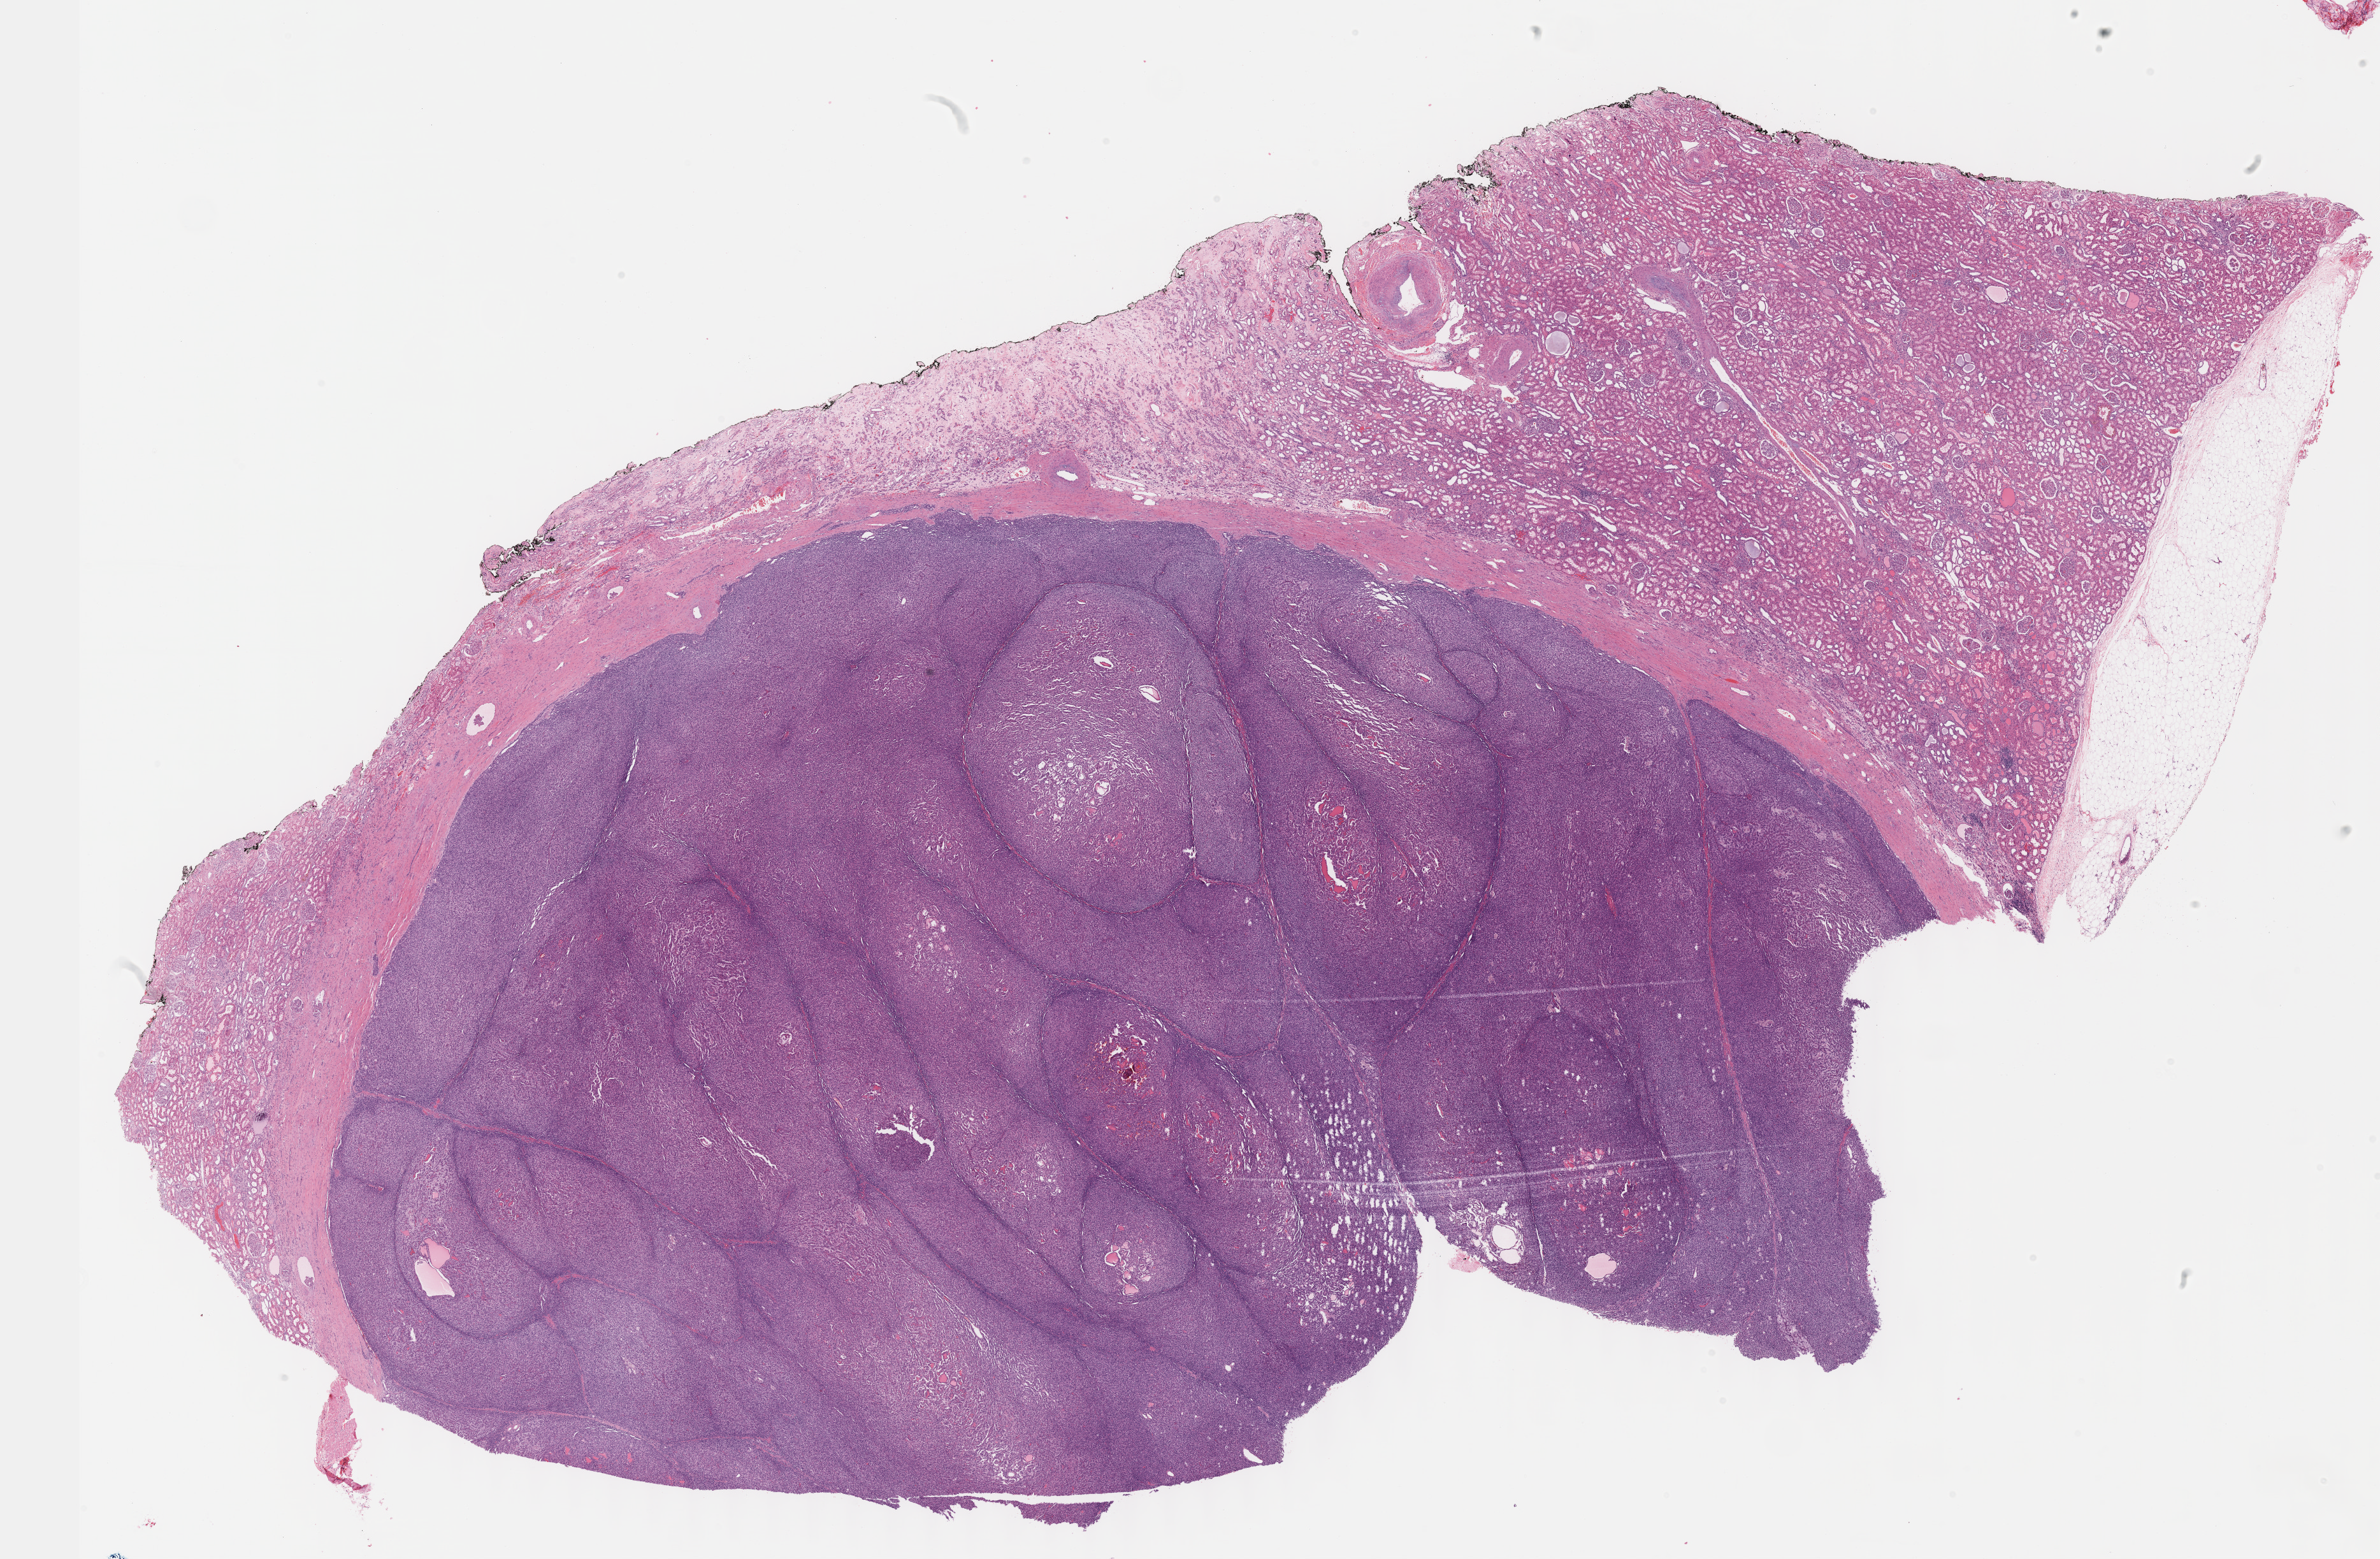
Digitized H&E-stained tissue section (whole slide) — whole scanned area (about 30.2 x 19.8 mm, acquisition: 40x scan) shown as a low-resolution overview; FFPE section; sample: primary tumour, kidney. Male patient.
Diagnosis: Papillary adenocarcinoma, NOS.